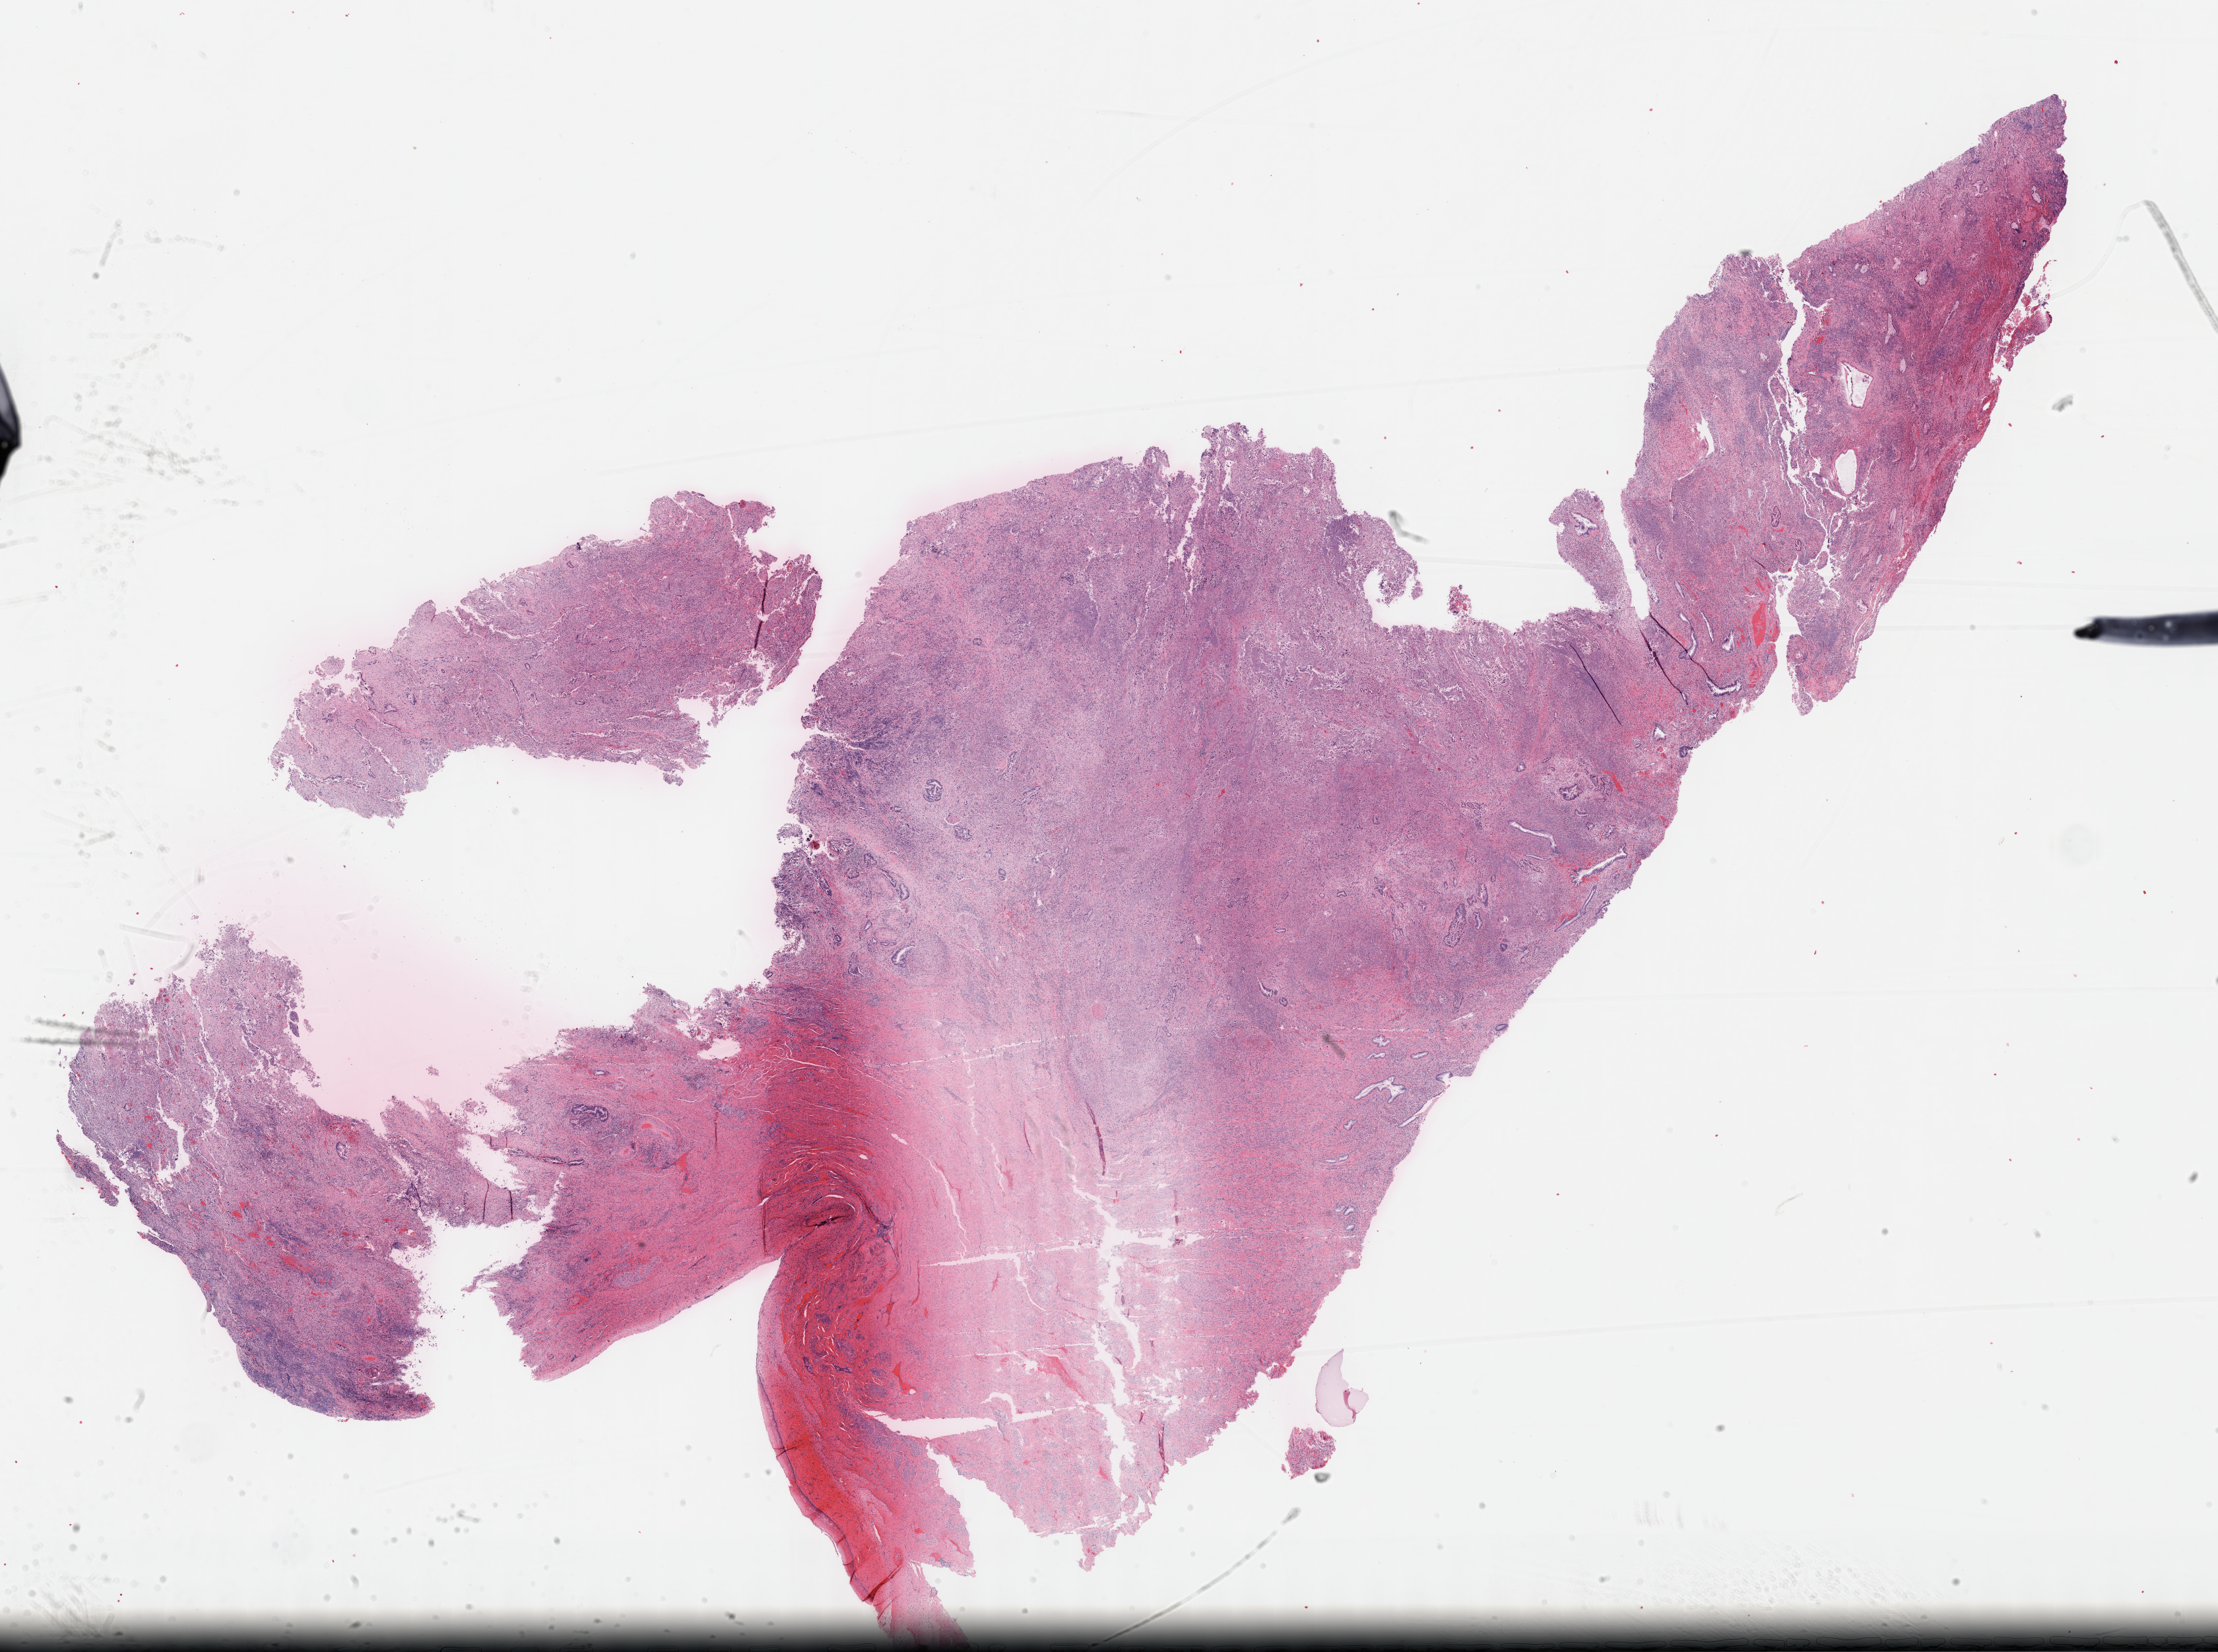
Whole-slide histology image, Hematoxylin and eosin (H&E) stained, a low-resolution overview of the entire scanned area, about 27.2 x 20.3 mm (acquisition: 40x scan), formalin-fixed paraffin-embedded (FFPE) diagnostic section, primary tumour sample from the pancreas. Female, age 66 years at initial diagnosis. Histologic grade: G2 (moderately differentiated).
AJCC pathologic stage: IV (7th edition). Pathologic diagnosis: Infiltrating duct carcinoma, NOS (body of pancreas). TNM: T3 N1 M1. Lymph nodes positive (case pathology): 1 of 12 examined.